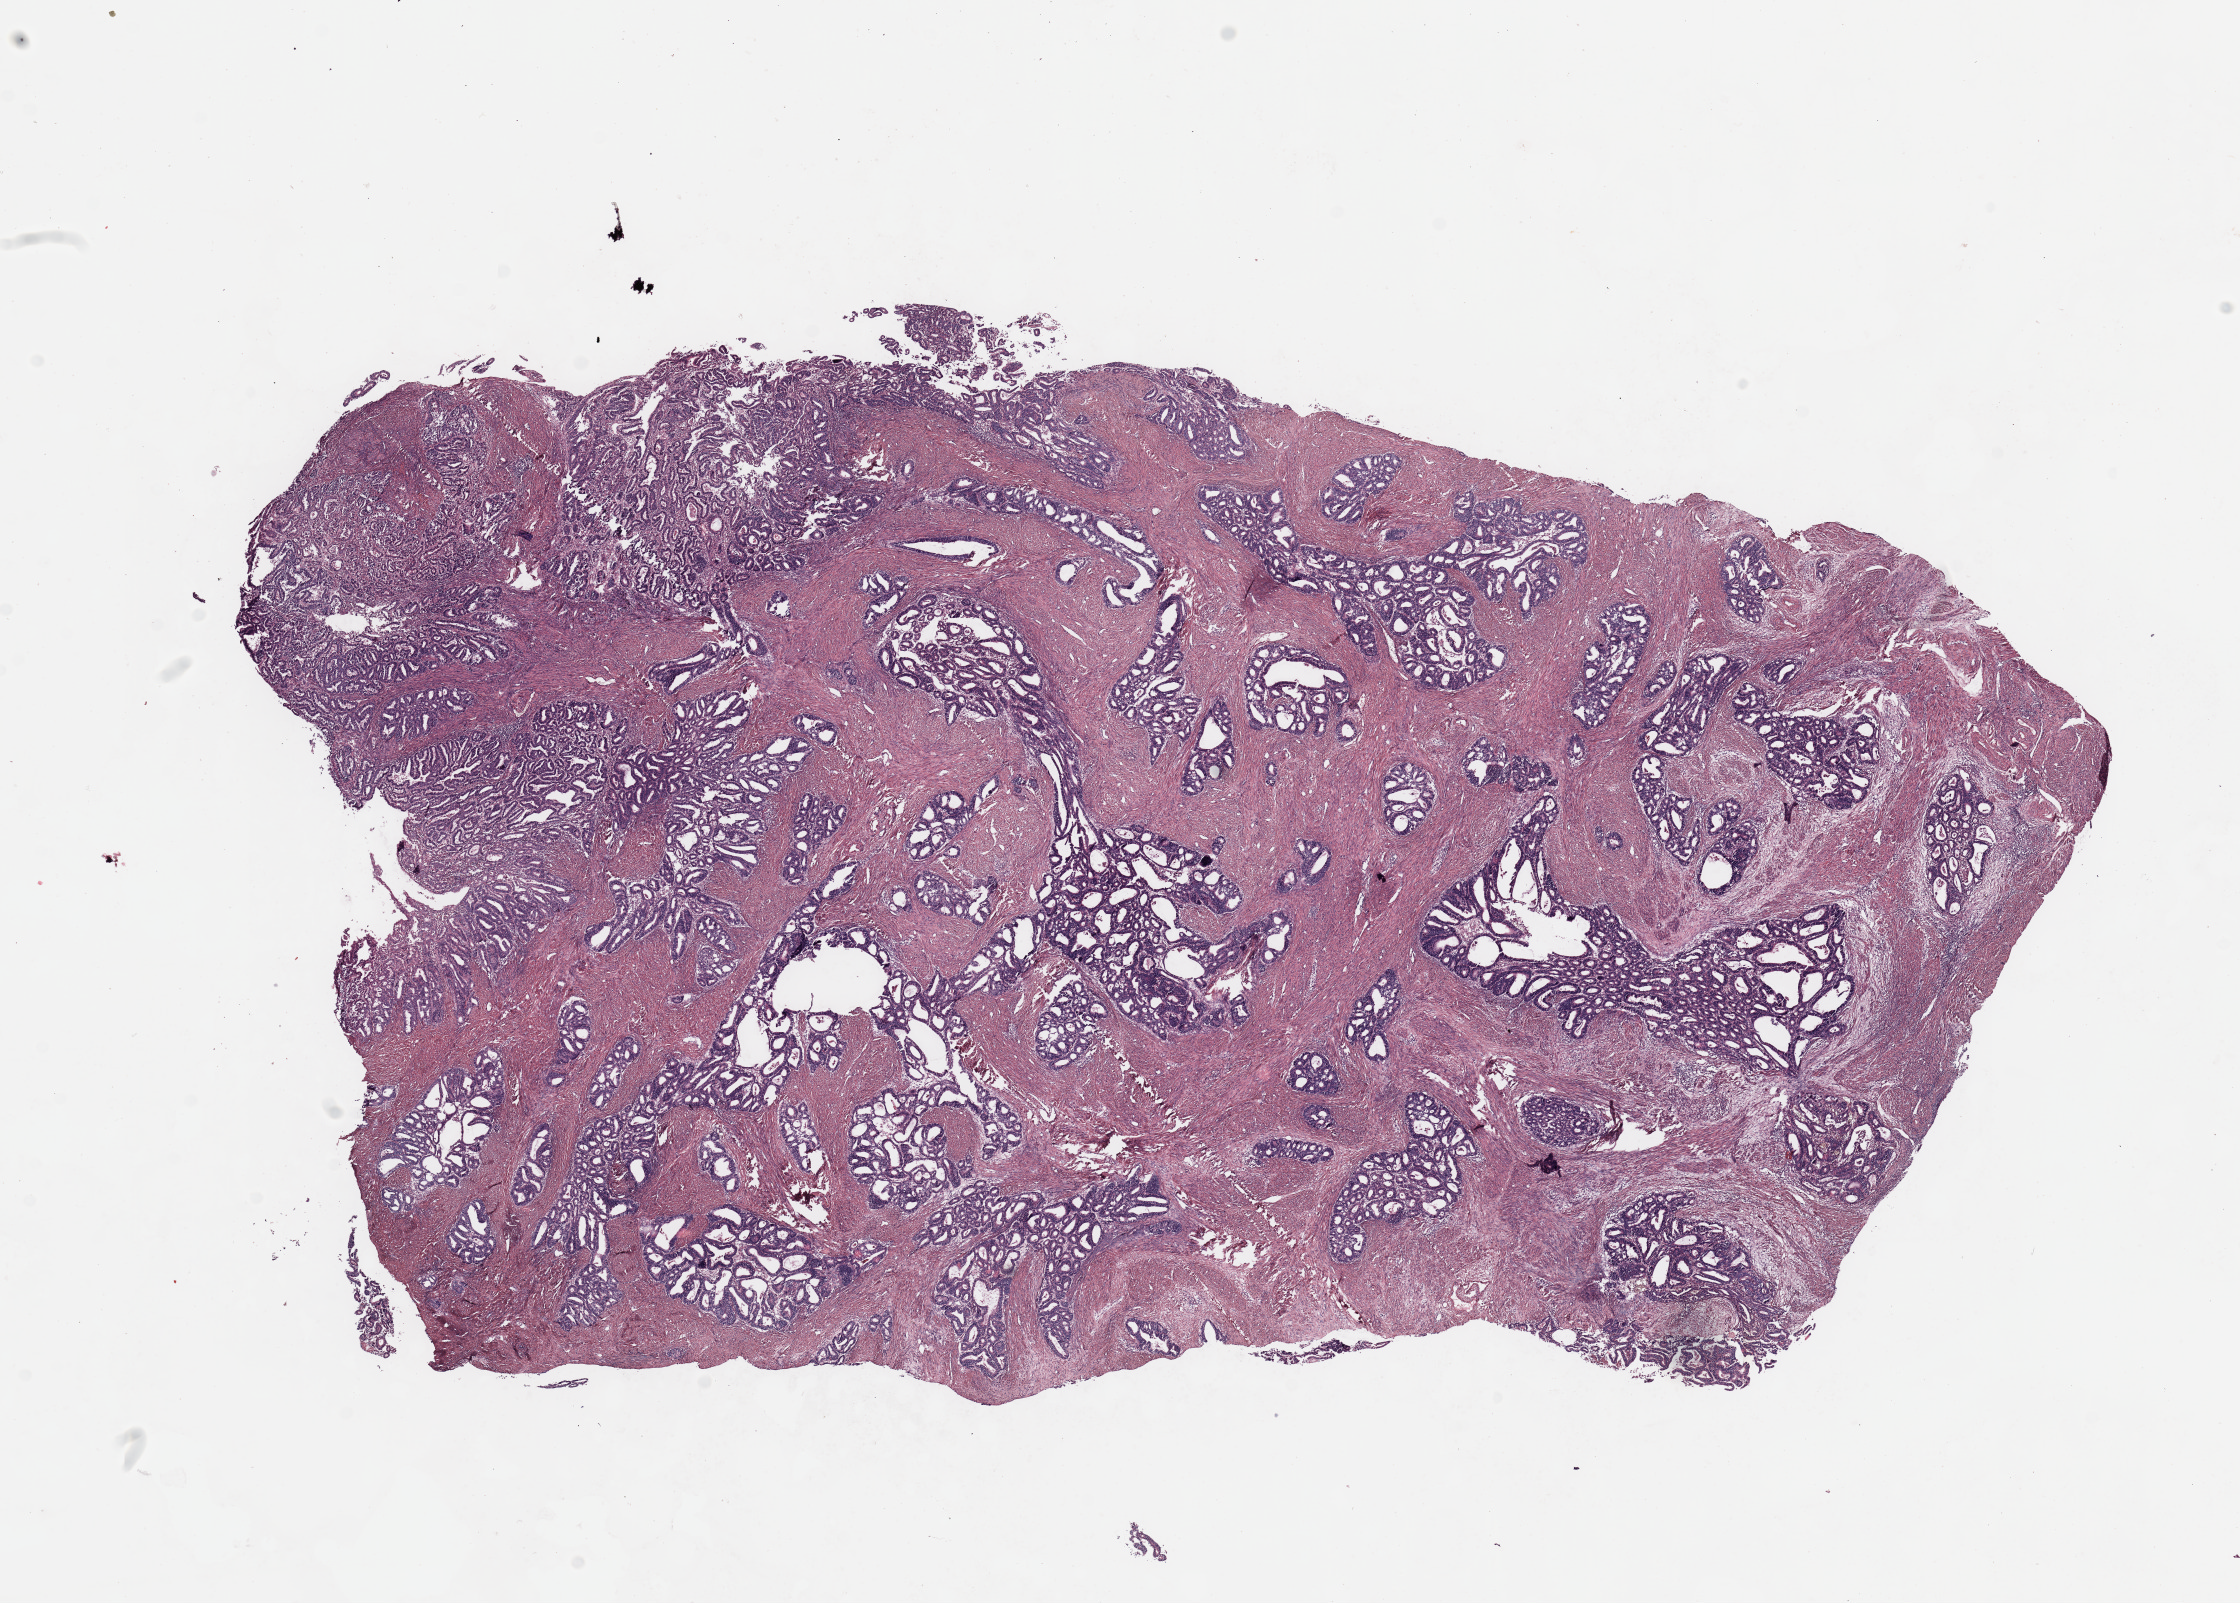
Digitized H&E-stained tissue section (whole slide), shown as a low-resolution overview of the whole scanned area (about 17.7 x 12.7 mm, slide scanned at 20x), uterus, tumour tissue. Patient: female, age 67 years. Histologic grade: G2 (moderately differentiated).
Histologic diagnosis: Endometrioid adenocarcinoma, NOS. AJCC pathologic stage: I.